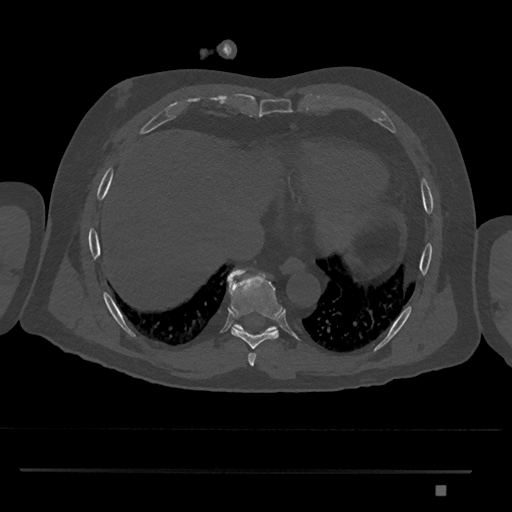
CT including the spine, one axial slice. Position 1097 of 1134 along the scan axis. Reconstruction kernel Br40s/3. 120 kVp. Bone window (W 1800 / L 400 HU). 512 × 512 image matrix, field of view 429 × 429 mm. Patient: male, 65 years. Case-level facts recorded for this patient, not image findings: primary cancer: prostate.
Annotated regions visible in this slice (semi-automatic segmentation, software-assisted and operator-edited):
- T8 vertebra: bounding box (x1, y1, x2, y2) in pixels: (228, 269, 284, 348)
- T9 vertebra: (231, 272, 277, 333)